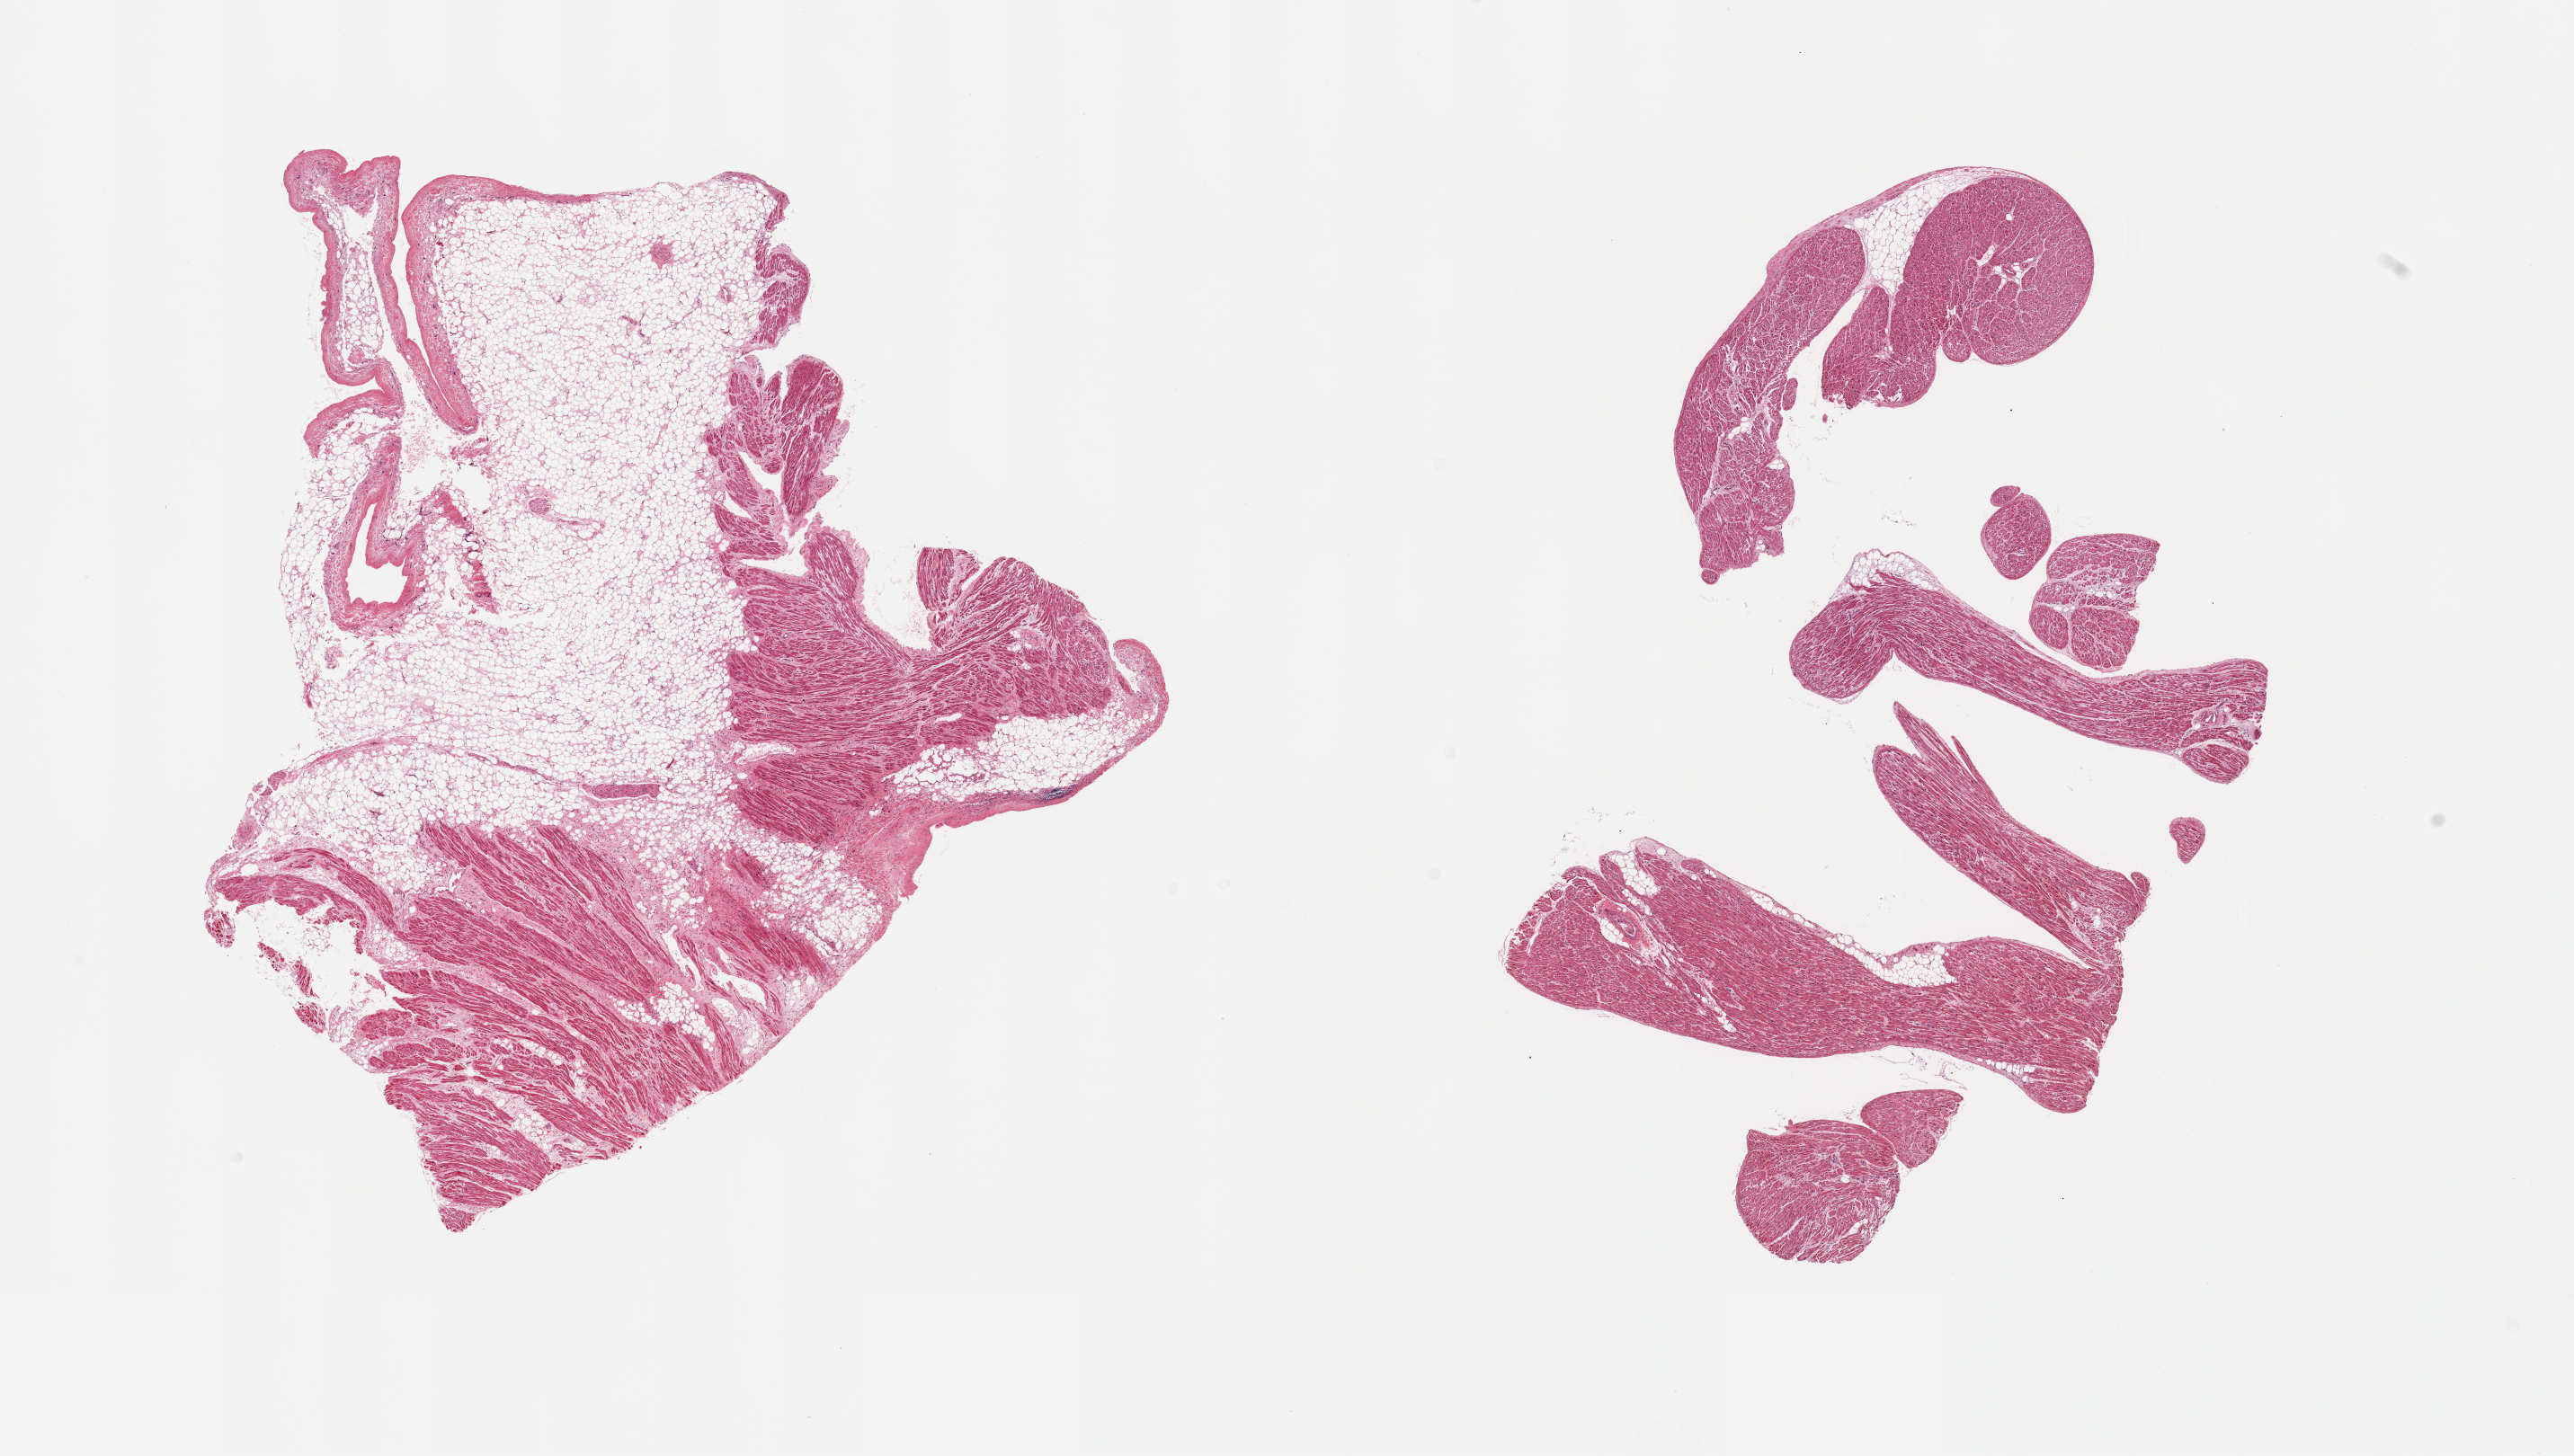
Digitized H&E-stained section, brightfield, a low-resolution overview of the entire scanned area, about 22.6 x 12.8 mm (from a 20x scan), PAXgene-fixed paraffin-embedded (PFPE) section, sampled site (target tissue): auricular appendage, donor tissue sample. Donor sex: female.
Review note (as recorded): 2 pieces; 1 with 60% internal & external fat; other <5% fat.